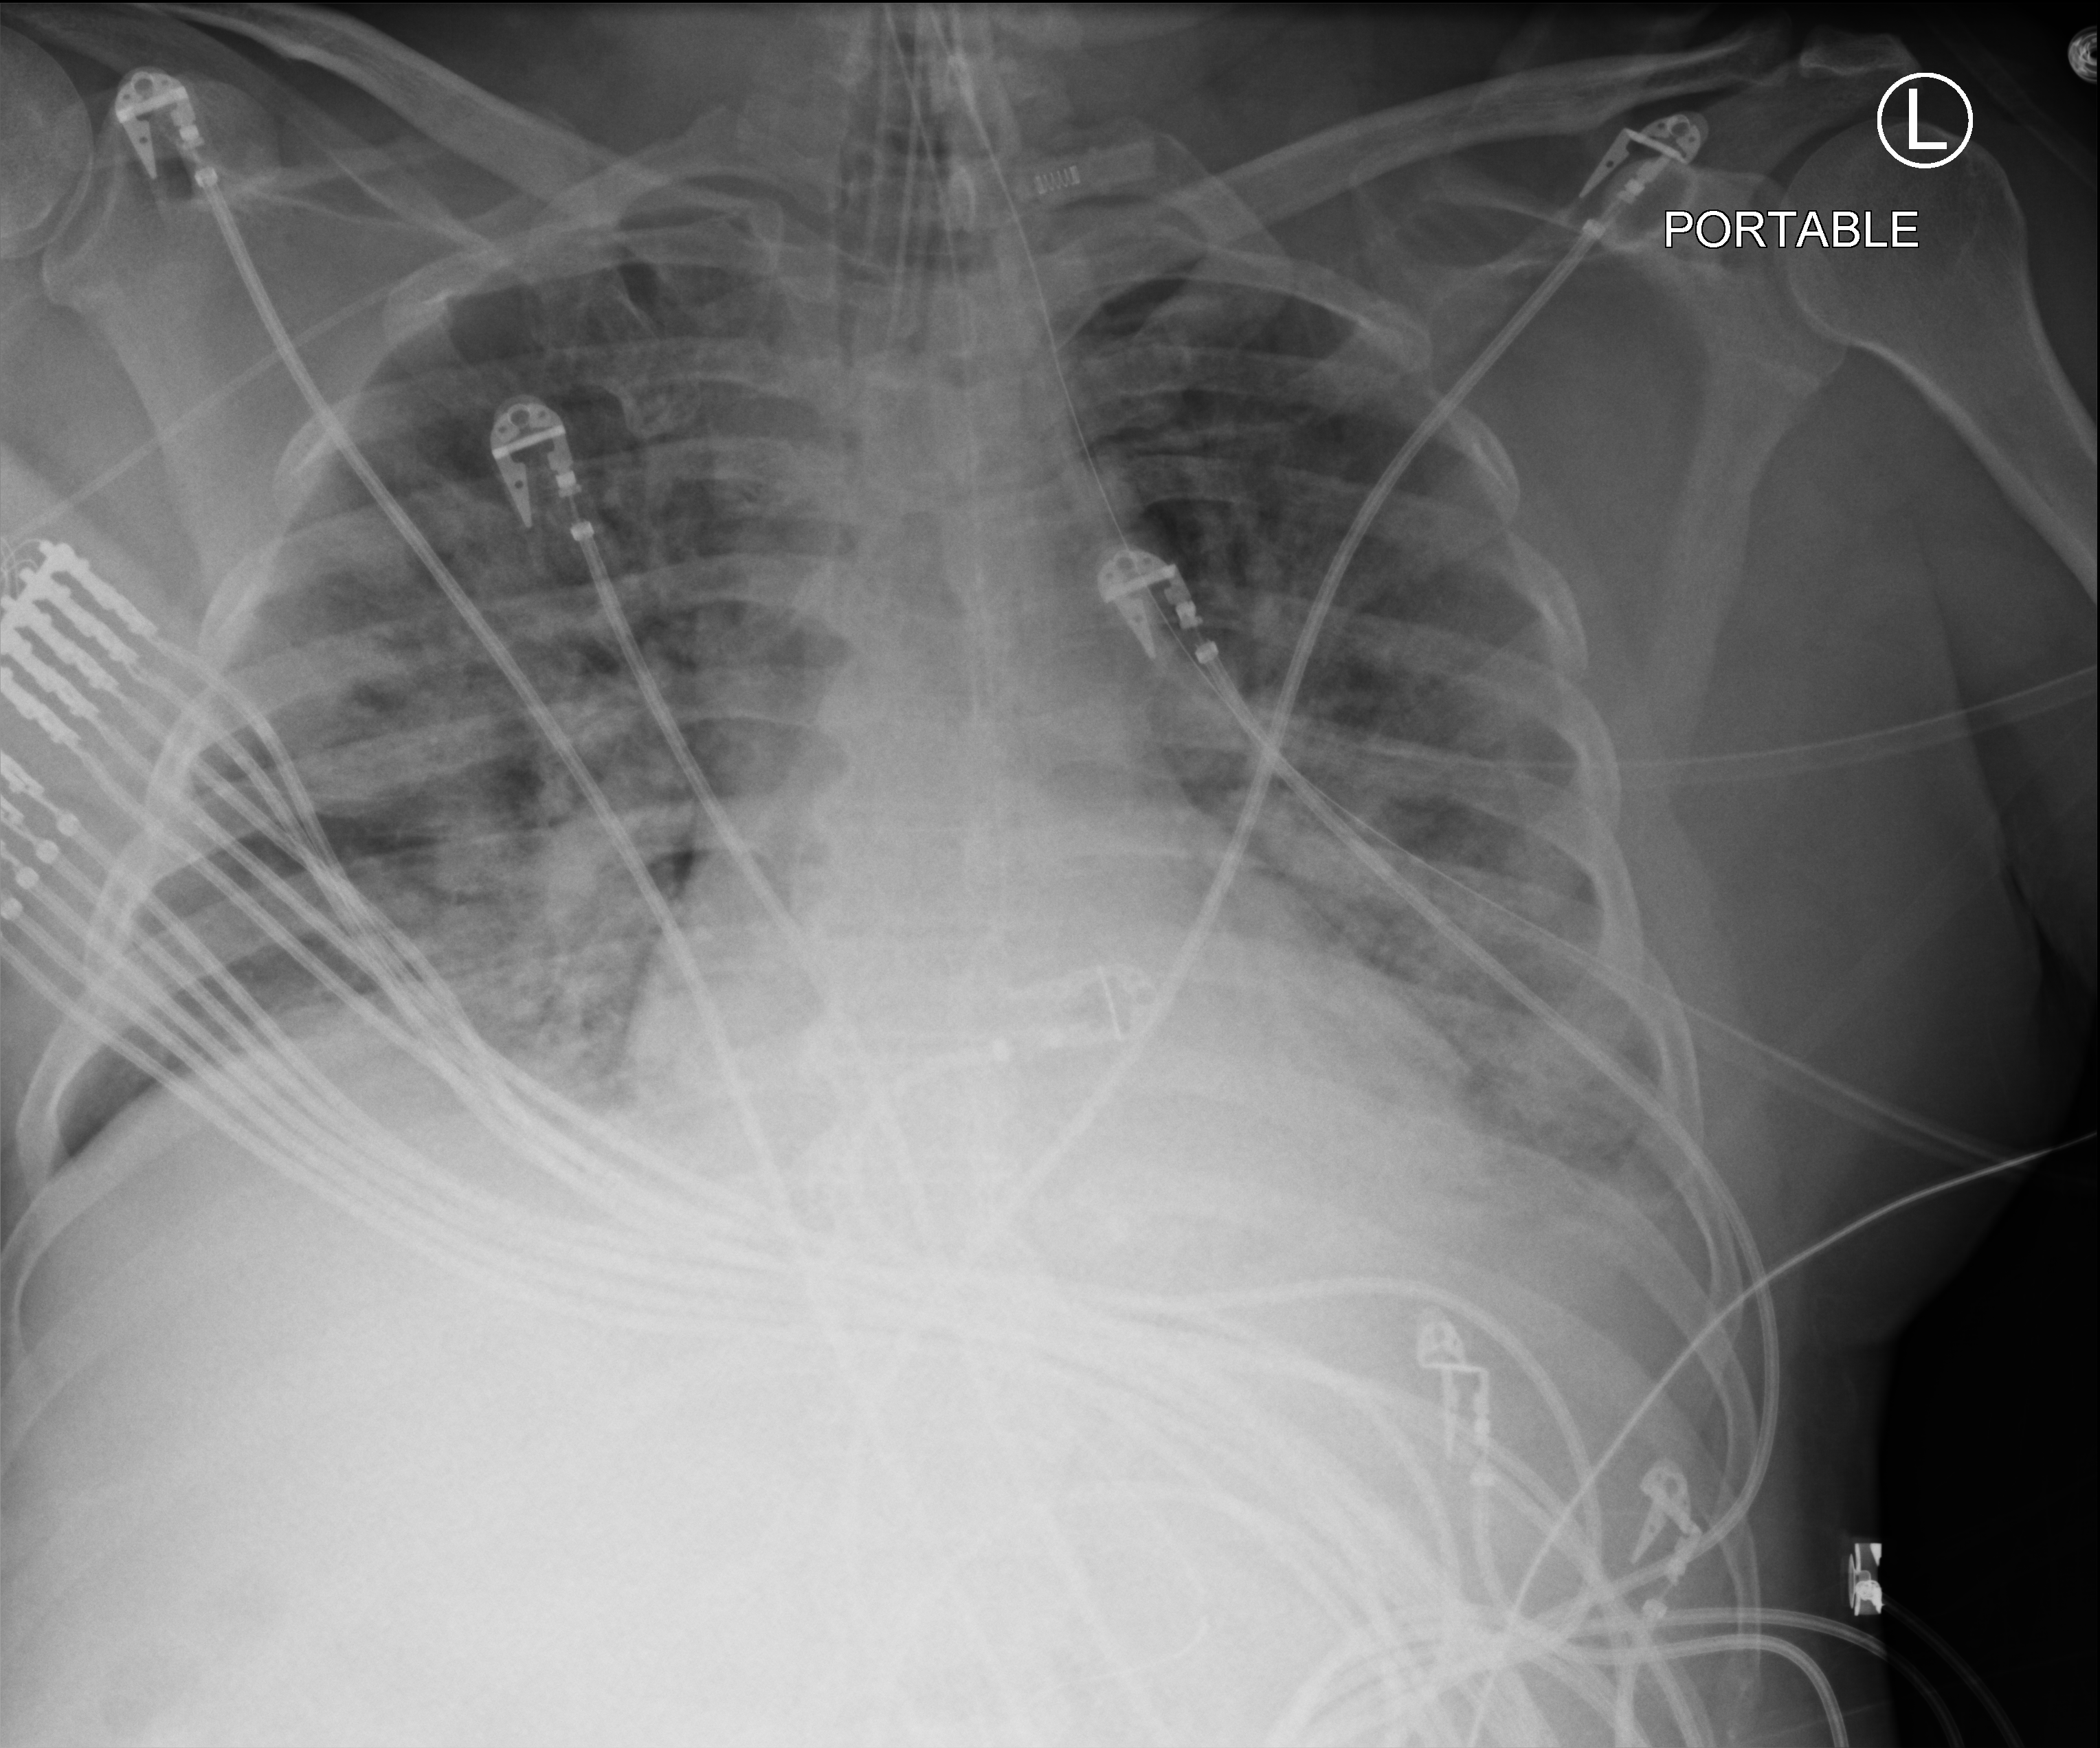
Portable chest radiograph; anteroposterior (AP) projection. Patient hospitalised with COVID-19; male, aged 18–59 years.
Admission-level facts for this patient (not findings on this image; timing relative to this image not recorded): hypertension (admission record): yes.